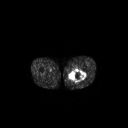
FDG PET of an extremity soft-tissue mass (from a PET/CT study), one axial slice. Slice 247 of 267 in the series (ordered by position). 128 × 128 image matrix, field of view 700 × 700 mm. Male patient, age 44 years. Case-level facts recorded for this patient, not image findings: histological type: undifferentiated pleomorphic liposarcoma; grade: high; site of the primary tumour: left thigh.
Structures marked on this image (expert contour drawn on MRI and transferred to this co-registered scan by the dataset authors):
- gross tumour volume including surrounding oedema: box from (x=67, y=69) to (x=86, y=83) px
- gross tumour volume (mass): (x=69, y=69)–(x=86, y=81)